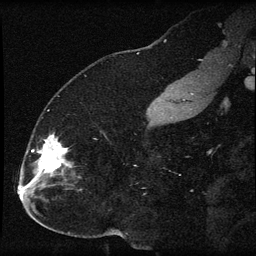
Breast MRI (dynamic contrast-enhanced), one sagittal slice. Position 27 of 60 along the scan axis. Dynamic contrast-enhanced series, image 2 of 3 at this slice position (ordered by acquisition). 1.5 T. TE 4.2 ms, TR 8.2 ms. 2 mm slice thickness. 256 × 256 image matrix, field of view 180 × 180 mm. Female patient, age 32 years.
Outlined on this slice (semi-automatically segmented with operator editing):
- analysis volume of interest (the breast-tissue region the enhancement analysis was run in; not a lesion): bounding box (x1, y1, x2, y2) in pixels: (31, 134, 79, 184)
- tumour enhancement mask (voxels above the 70 % enhancement threshold inside the analysis volume of interest): (31, 135, 68, 183)